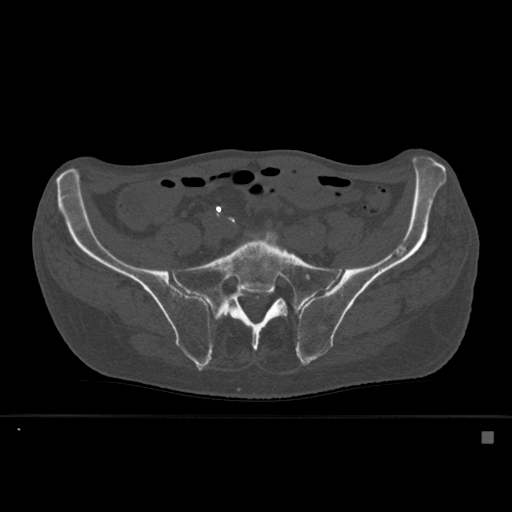
CT including the spine, one axial slice. Position 155 of 527 along the scan axis. Bone window (W 1800 / L 400 HU). 1.5 mm slice thickness. 512 × 512 image matrix, field of view 373 × 373 mm. Patient: male, 78 years. From the clinical record (not read from this slice): primary cancer: prostate.
Annotated regions visible in this slice (semi-automatically segmented with operator editing):
- L5 vertebra: box from (x=283, y=304) to (x=288, y=312) px